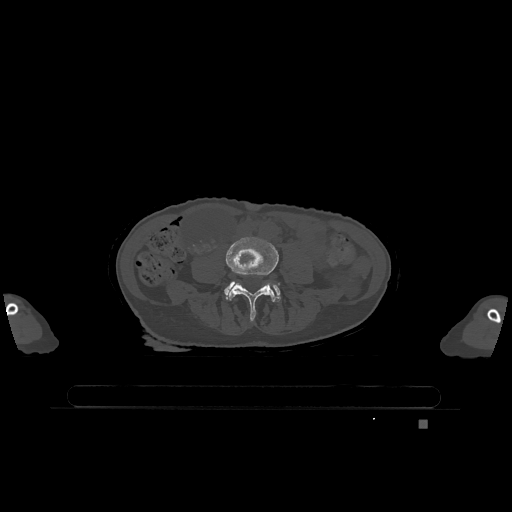
CT including the spine, one axial slice; position 287 of 1317 along the scan axis; bone window (W 1800 / L 400 HU); 0.5 mm slice thickness; 512 × 512 image matrix. Patient: female, 74 years. From the clinical record (not read from this slice): primary cancer: lung; vertebrae with lytic lesions (as recorded): T1, T4, T5, T6, L4, L5.
Annotated regions visible in this slice (semi-automatic segmentation, software-assisted and operator-edited):
- L4 vertebra: bounding box (x1, y1, x2, y2) in pixels: (226, 235, 280, 321)
- L5 vertebra: (224, 281, 281, 302)